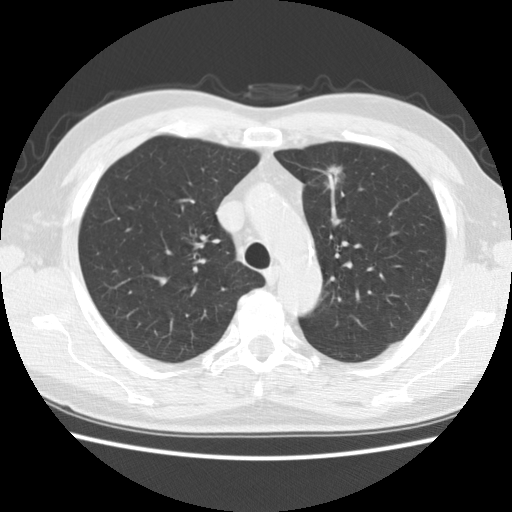
Low-dose screening chest CT, one axial slice. Position 125 of 172 along the scan axis. 120 kVp. Lung window (W 1500 / L -600 HU). 2.5 mm slice thickness. 512 × 512 image matrix, field of view 337 × 337 mm.
Outlined on this slice (outlined manually by an expert reader):
- lesion 1 (tumor, upper lobe of left lung): bounding box (x1, y1, x2, y2) in pixels: (328, 166, 342, 184)